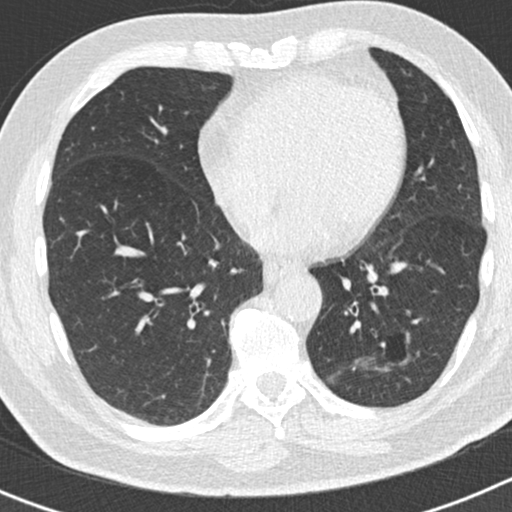
Low-dose screening chest CT, axial slice, second screening round (one year after baseline), lung window (W 1500 / L -600 HU), 2 mm slice thickness, 120 kVp, slice 103 of 186 in the series. Male, age 66 years at enrolment.
Expert-annotated lung lesion, bounding box [x1, y1, x2, y2] px = [345, 321, 418, 402]. Reader record for this screening exam (exam-level; its link to the box is not recorded): non-calcified nodule or mass ≥4 mm, left lower lobe, 50 × 33 mm, smooth margins, pre-existing on the prior screen: yes; interval growth: yes.